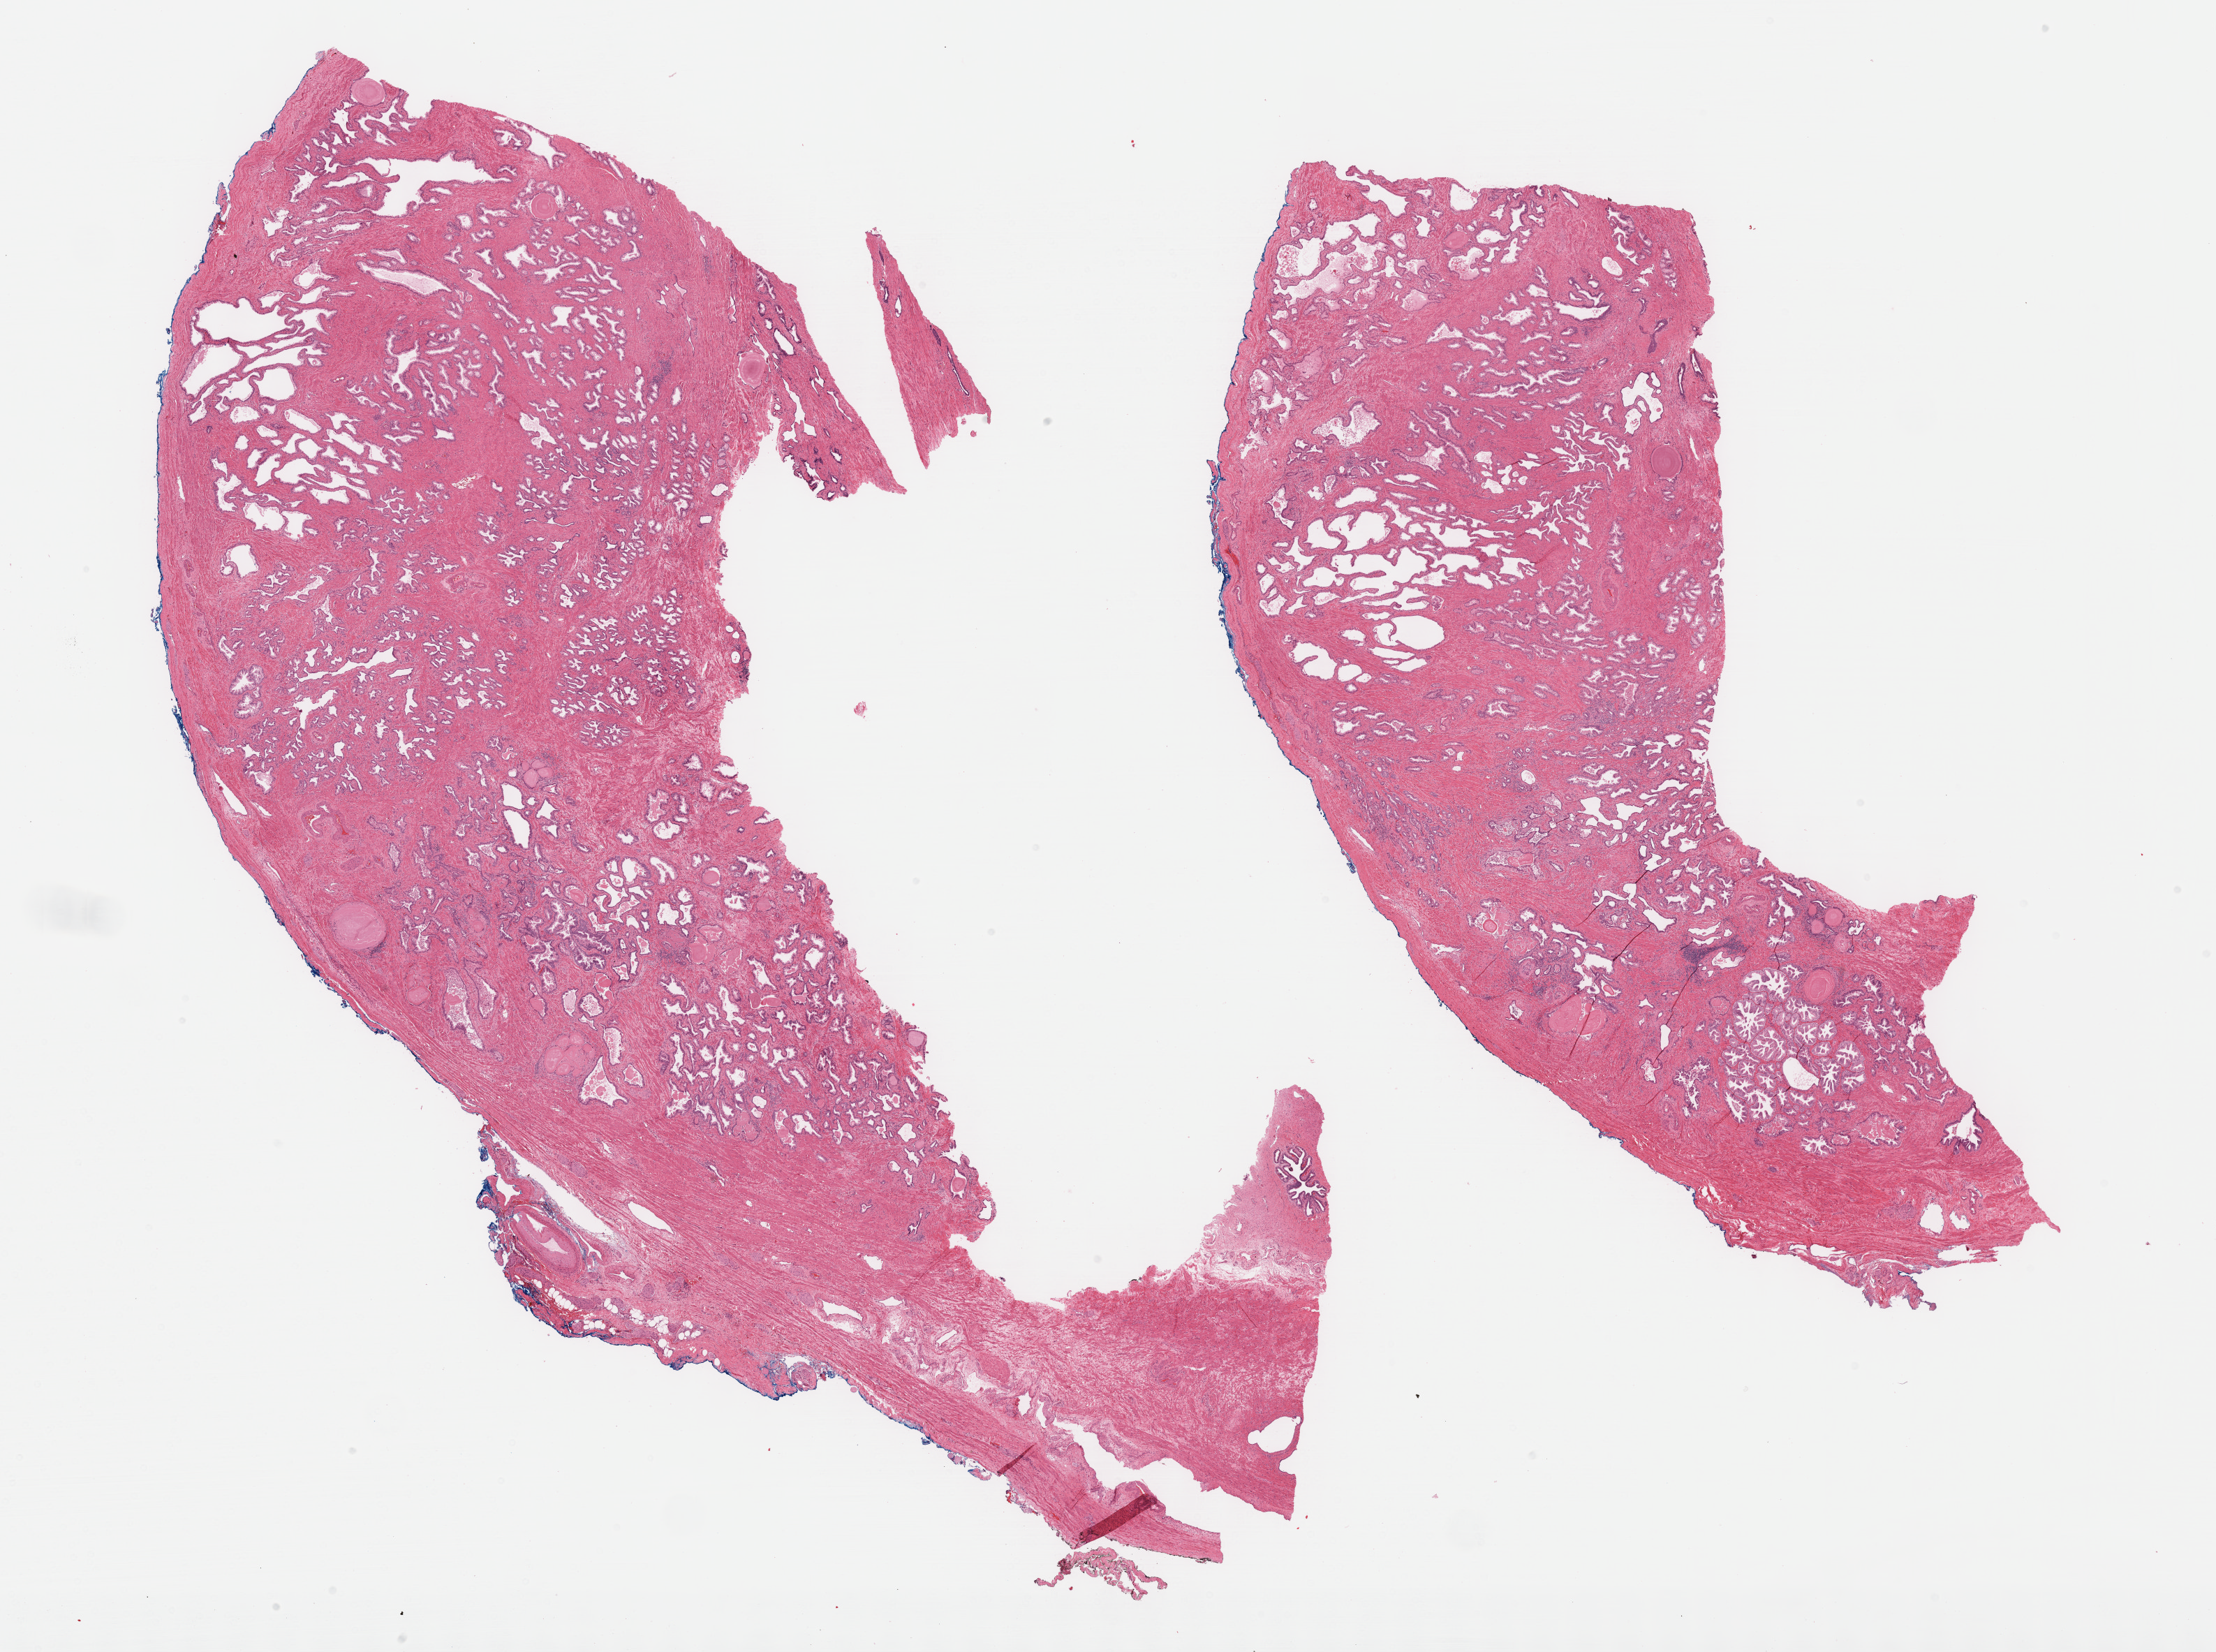
Whole-slide histology image, Hematoxylin and eosin (H&E) stained — low-resolution overview of the scanned area, about 25.7 x 19.1 mm (slide scanned at 40x); formalin-fixed paraffin-embedded (FFPE) diagnostic section; primary tumour sample from the prostate. Patient: male, age at initial diagnosis 61 years. Gleason score: 7 (3+4).
Laterality: bilateral. Diagnosis: Adenocarcinoma, NOS.